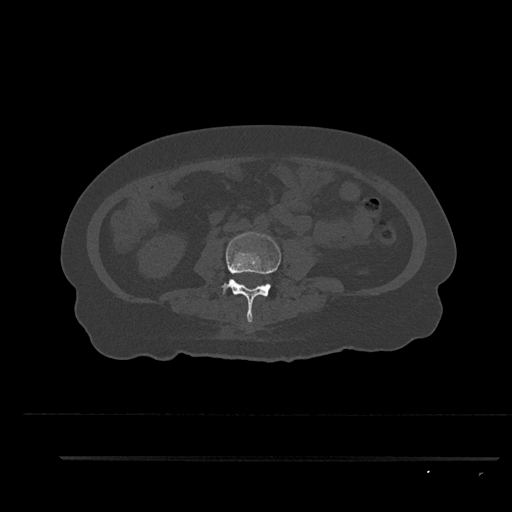
CT including the spine, one axial slice. Position 80 of 797 along the scan axis. Reconstruction kernel Br40s/3. 120 kVp. Bone window (W 1800 / L 400 HU). 0.5 mm slice thickness. 512 × 512 image matrix. Patient: female, 44 years. From the clinical record (not read from this slice): primary cancer: renal.
Annotated regions visible in this slice (semi-automatically segmented with operator editing):
- L3 vertebra: bounding box <220,231,281,323> (left, top, right, bottom; pixels)